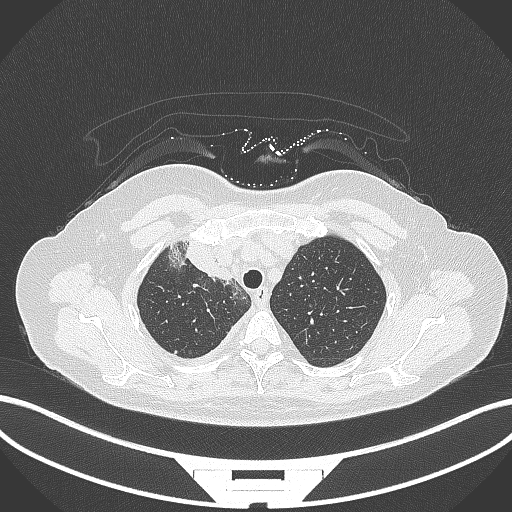
Chest CT, one axial slice; position 252 of 305 along the scan axis; reconstruction kernel B70f; 120 kVp; lung window (W 1500 / L -600 HU); 512 × 512 image matrix, field of view 400 × 400 mm. Female patient, age 52 years. From the clinical record (not read from this slice): clinical TNM (as recorded): T3 N1 M1.
Structures marked on this image (rectangle marked by the reading radiologist):
- lung tumour (recorded histology: adenocarcinoma): bounding box <168,235,233,286> (left, top, right, bottom; pixels)